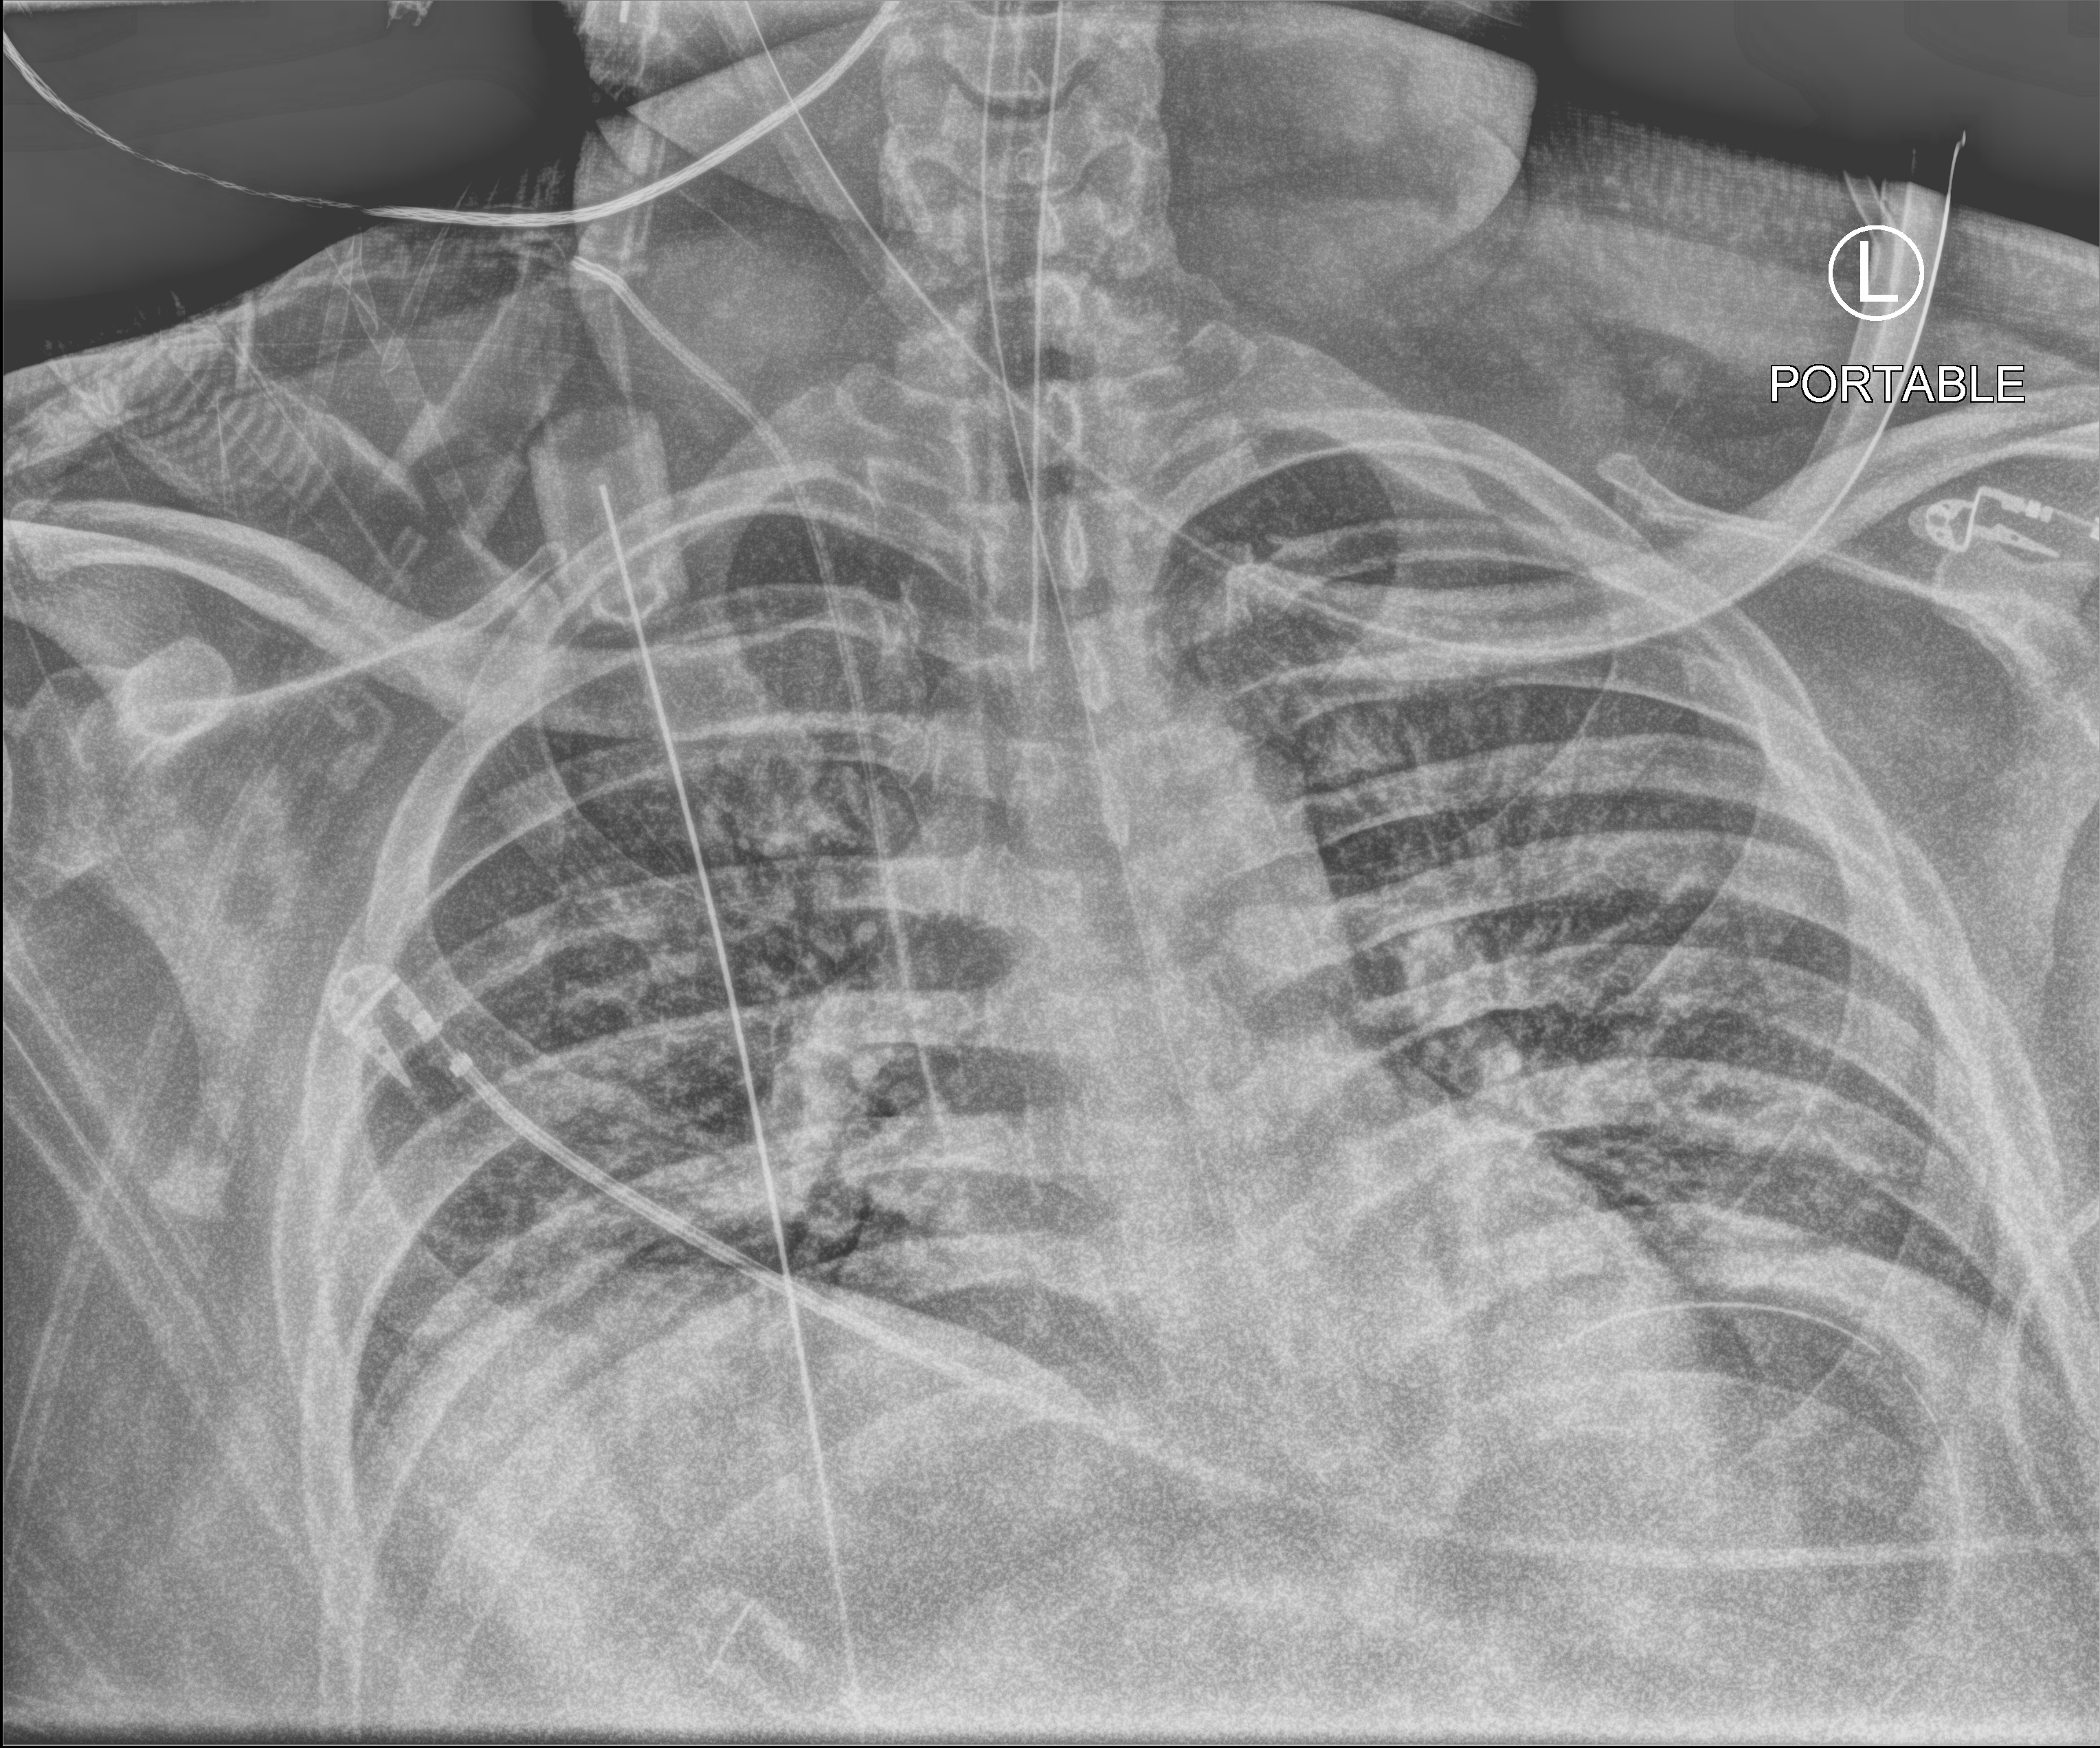
Portable chest radiograph; anteroposterior (AP) projection. Patient hospitalised with COVID-19; male, aged 18–59 years.
From the hospital-stay record, not from the radiograph (when in the stay this image was taken is not recorded):
- admitted to intensive care during this hospital stay: yes
- mechanically ventilated during this hospital stay: yes